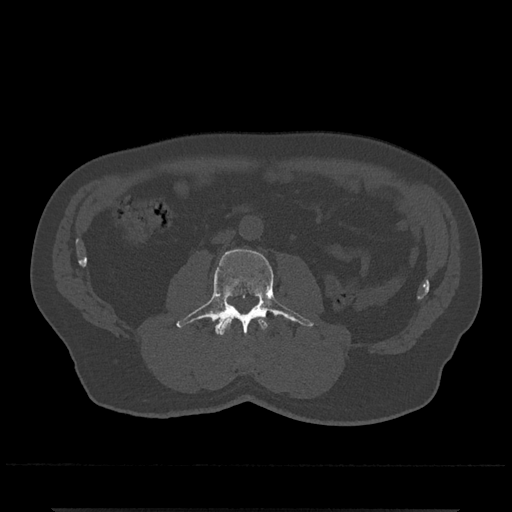
CT including the spine, one axial slice. Slice 229 of 797 in the series (ordered by position). Bone window (W 1800 / L 400 HU). 0.5 mm slice thickness. 512 × 512 image matrix, field of view 393 × 393 mm. Patient: male, 67 years. Case-level facts recorded for this patient, not image findings: primary cancer: prostate.
Structures marked on this image (semi-automatically segmented with operator editing):
- L2 vertebra: bounding box <218,317,268,335> (left, top, right, bottom; pixels)
- L3 vertebra: <176,249,313,334>